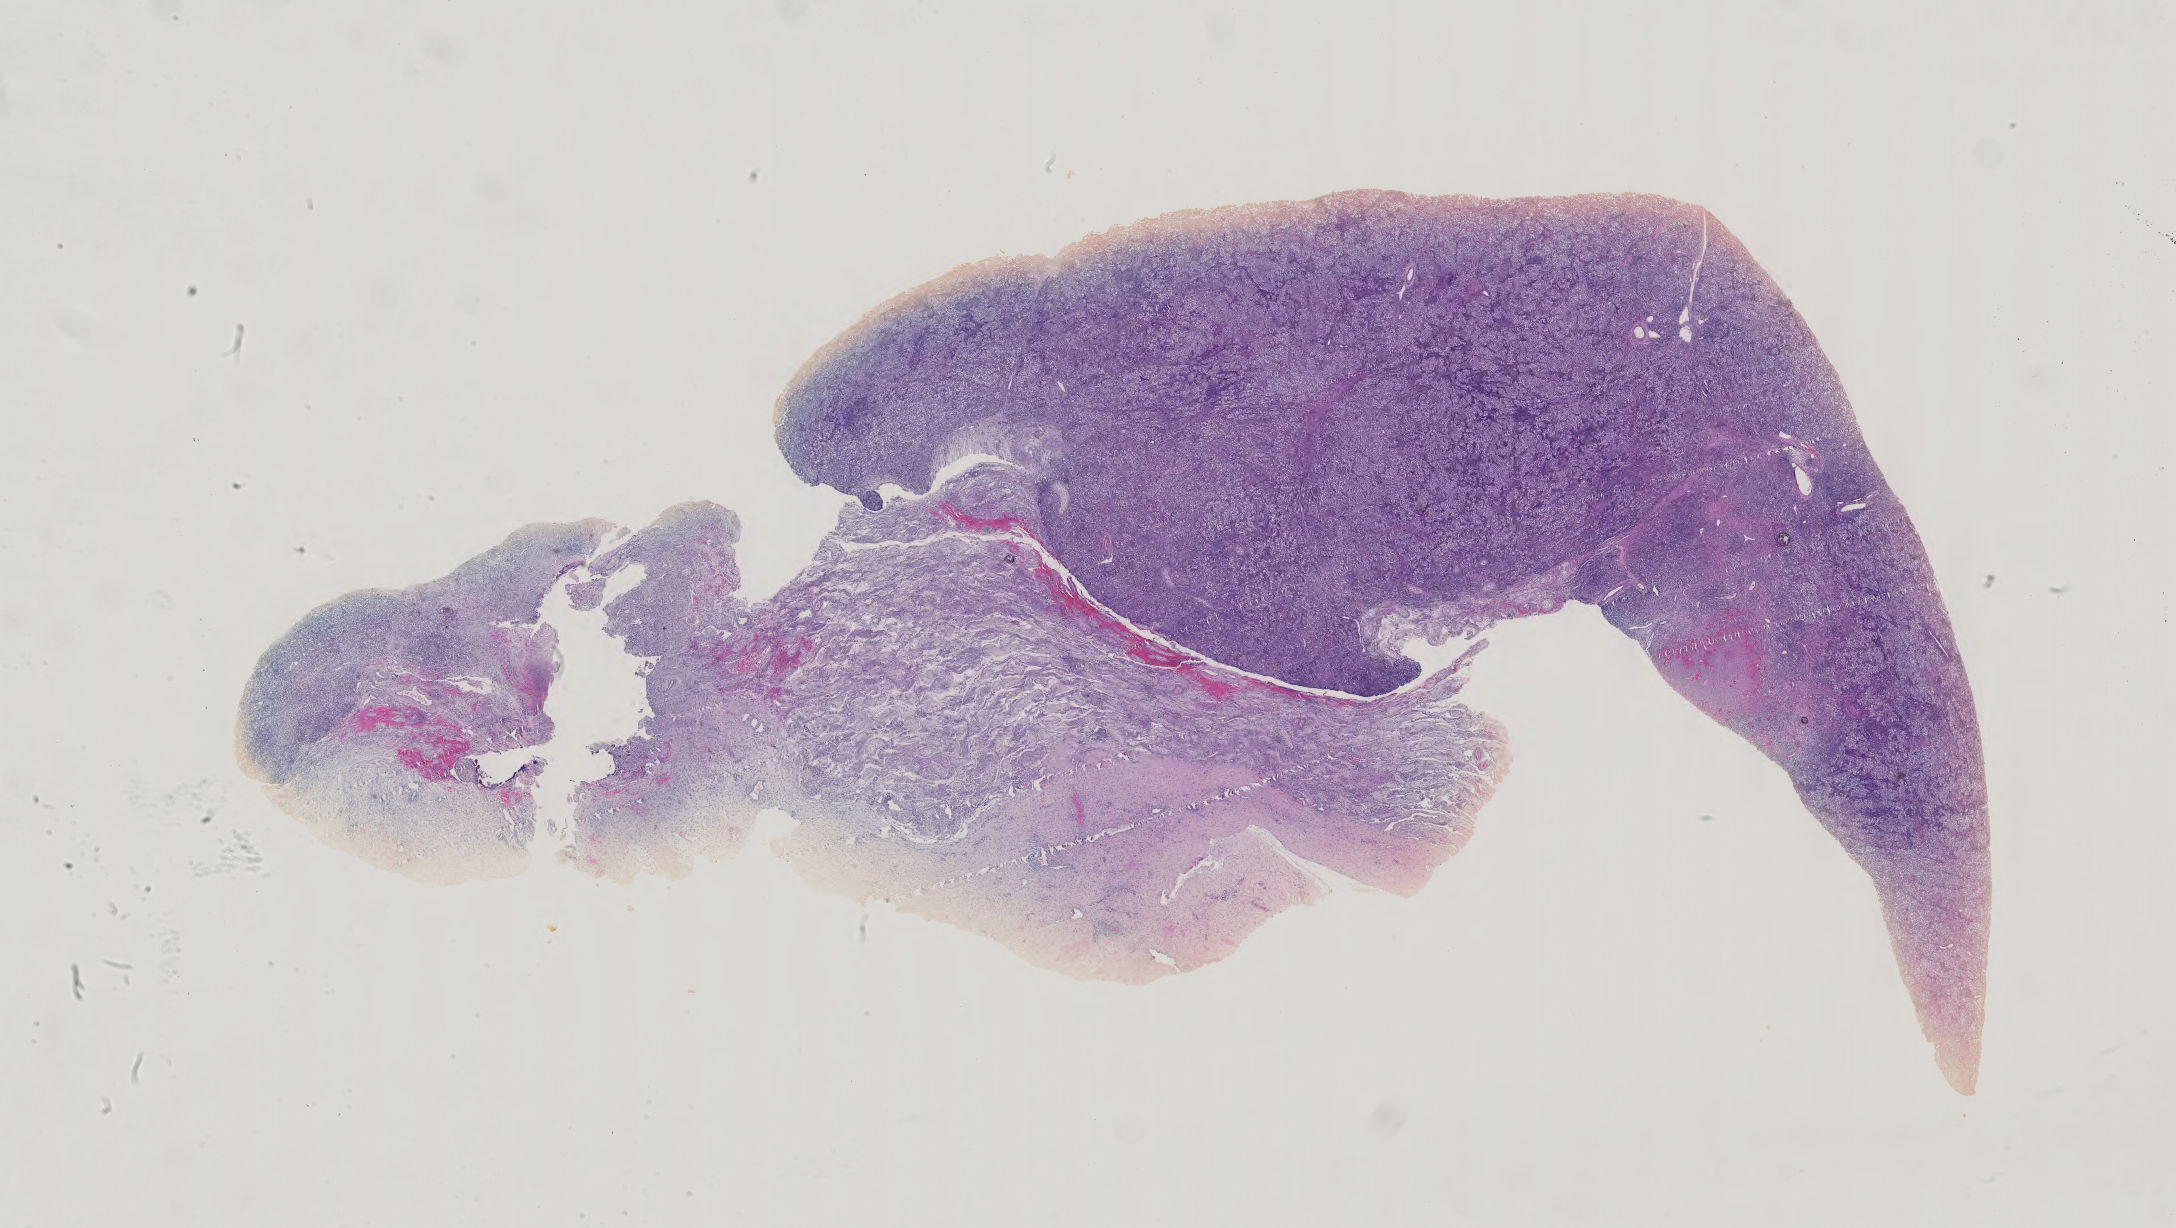
Digitized H&E tissue section (whole slide), a low-resolution overview of the entire scanned area, about 31.7 x 17.9 mm (from a 40x scan). Male patient.
Specimen: formalin-fixed paraffin-embedded (FFPE) diagnostic section; testis, primary tumour sample.